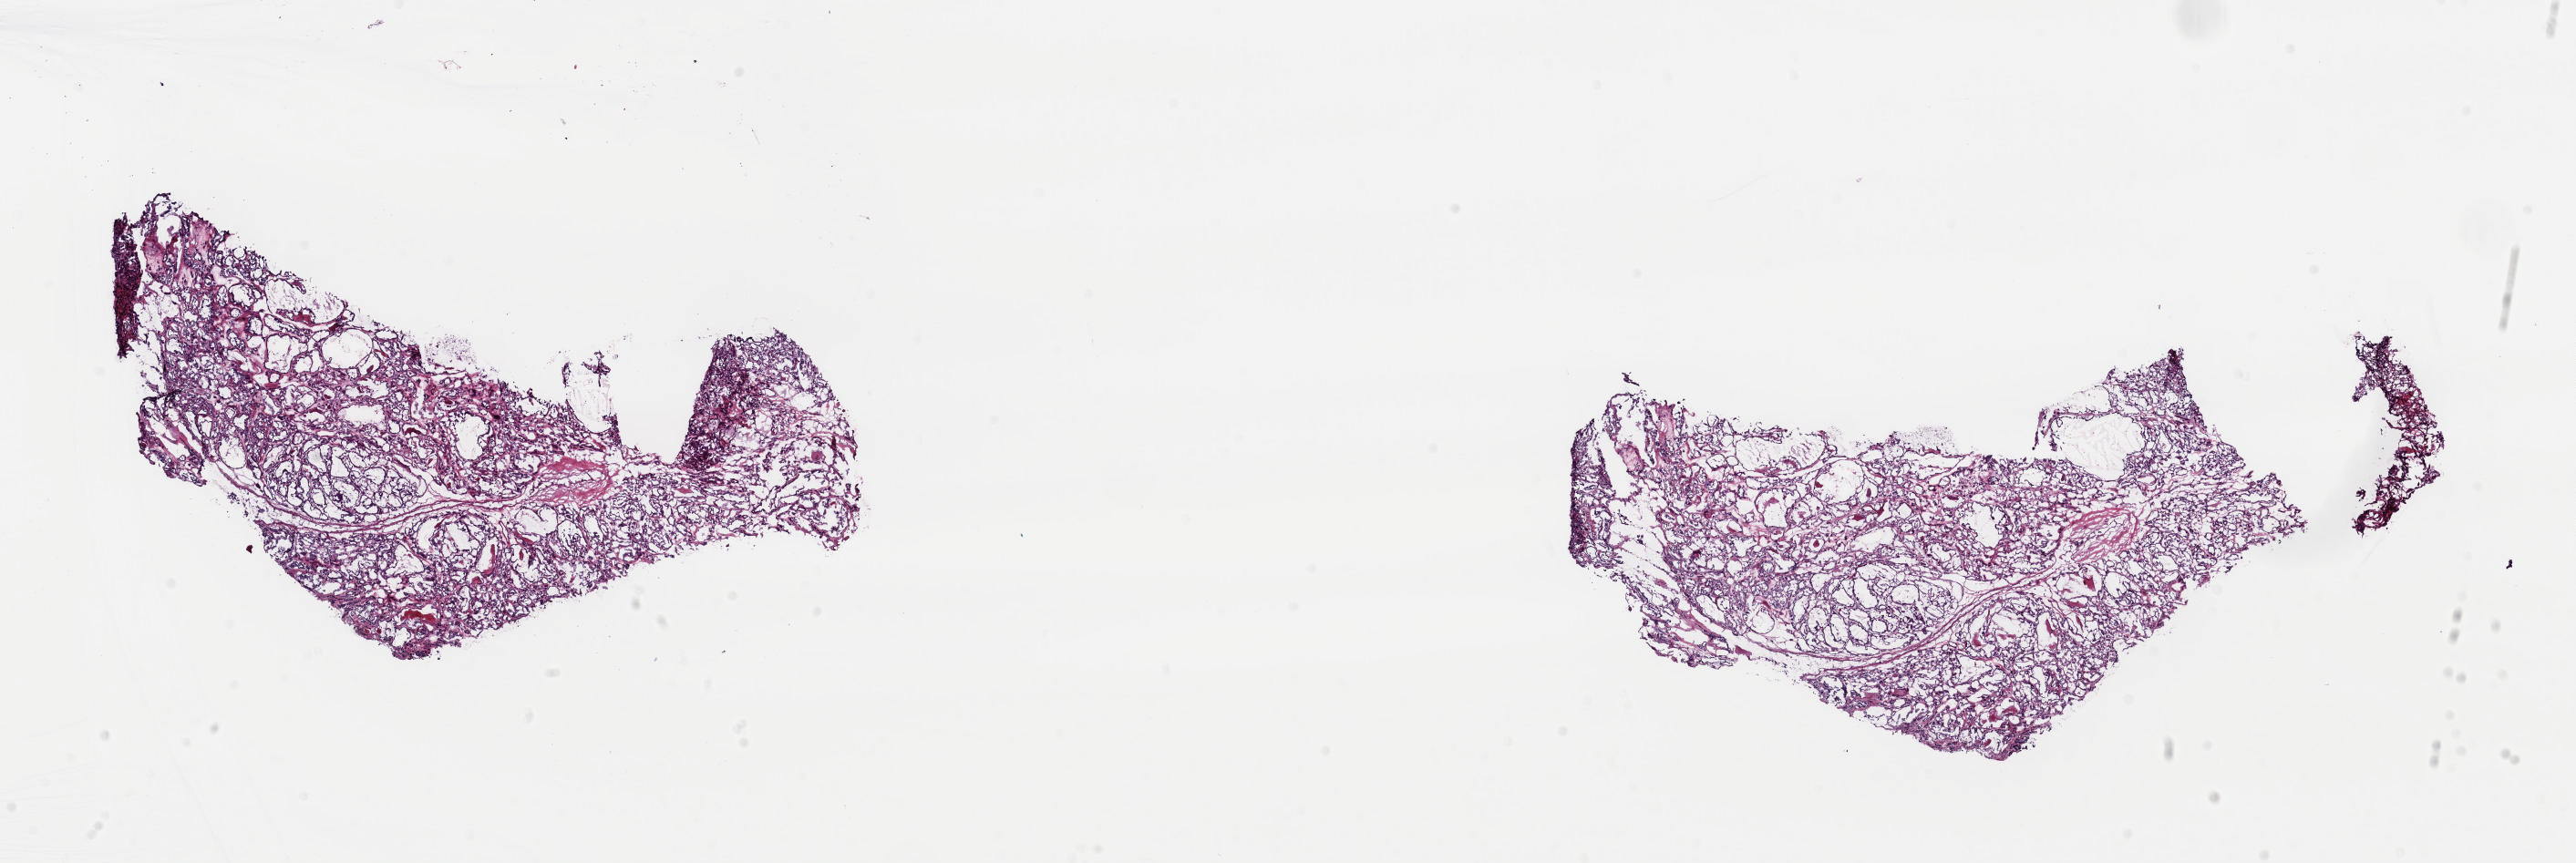
Digitized H&E-stained tissue section (whole slide), whole scanned area (about 22.3 x 7.5 mm, acquisition: 40x scan) shown as a low-resolution overview, frozen section from the top of the tissue portion, primary tumour sample from the thyroid. Patient: female, age at initial diagnosis 66 years. Pathologist review of this section (percent, as recorded): tumour cells 100%, tumour nuclei 85%, normal cells 0%, stromal cells 0%, necrosis 0%. Infiltration values recorded for this section: lymphocyte infiltration 0%, monocyte infiltration 0%, neutrophil infiltration 0%.
• diagnosis: Papillary adenocarcinoma, NOS (thyroid gland)
• AJCC pathologic stage: I (4th edition)